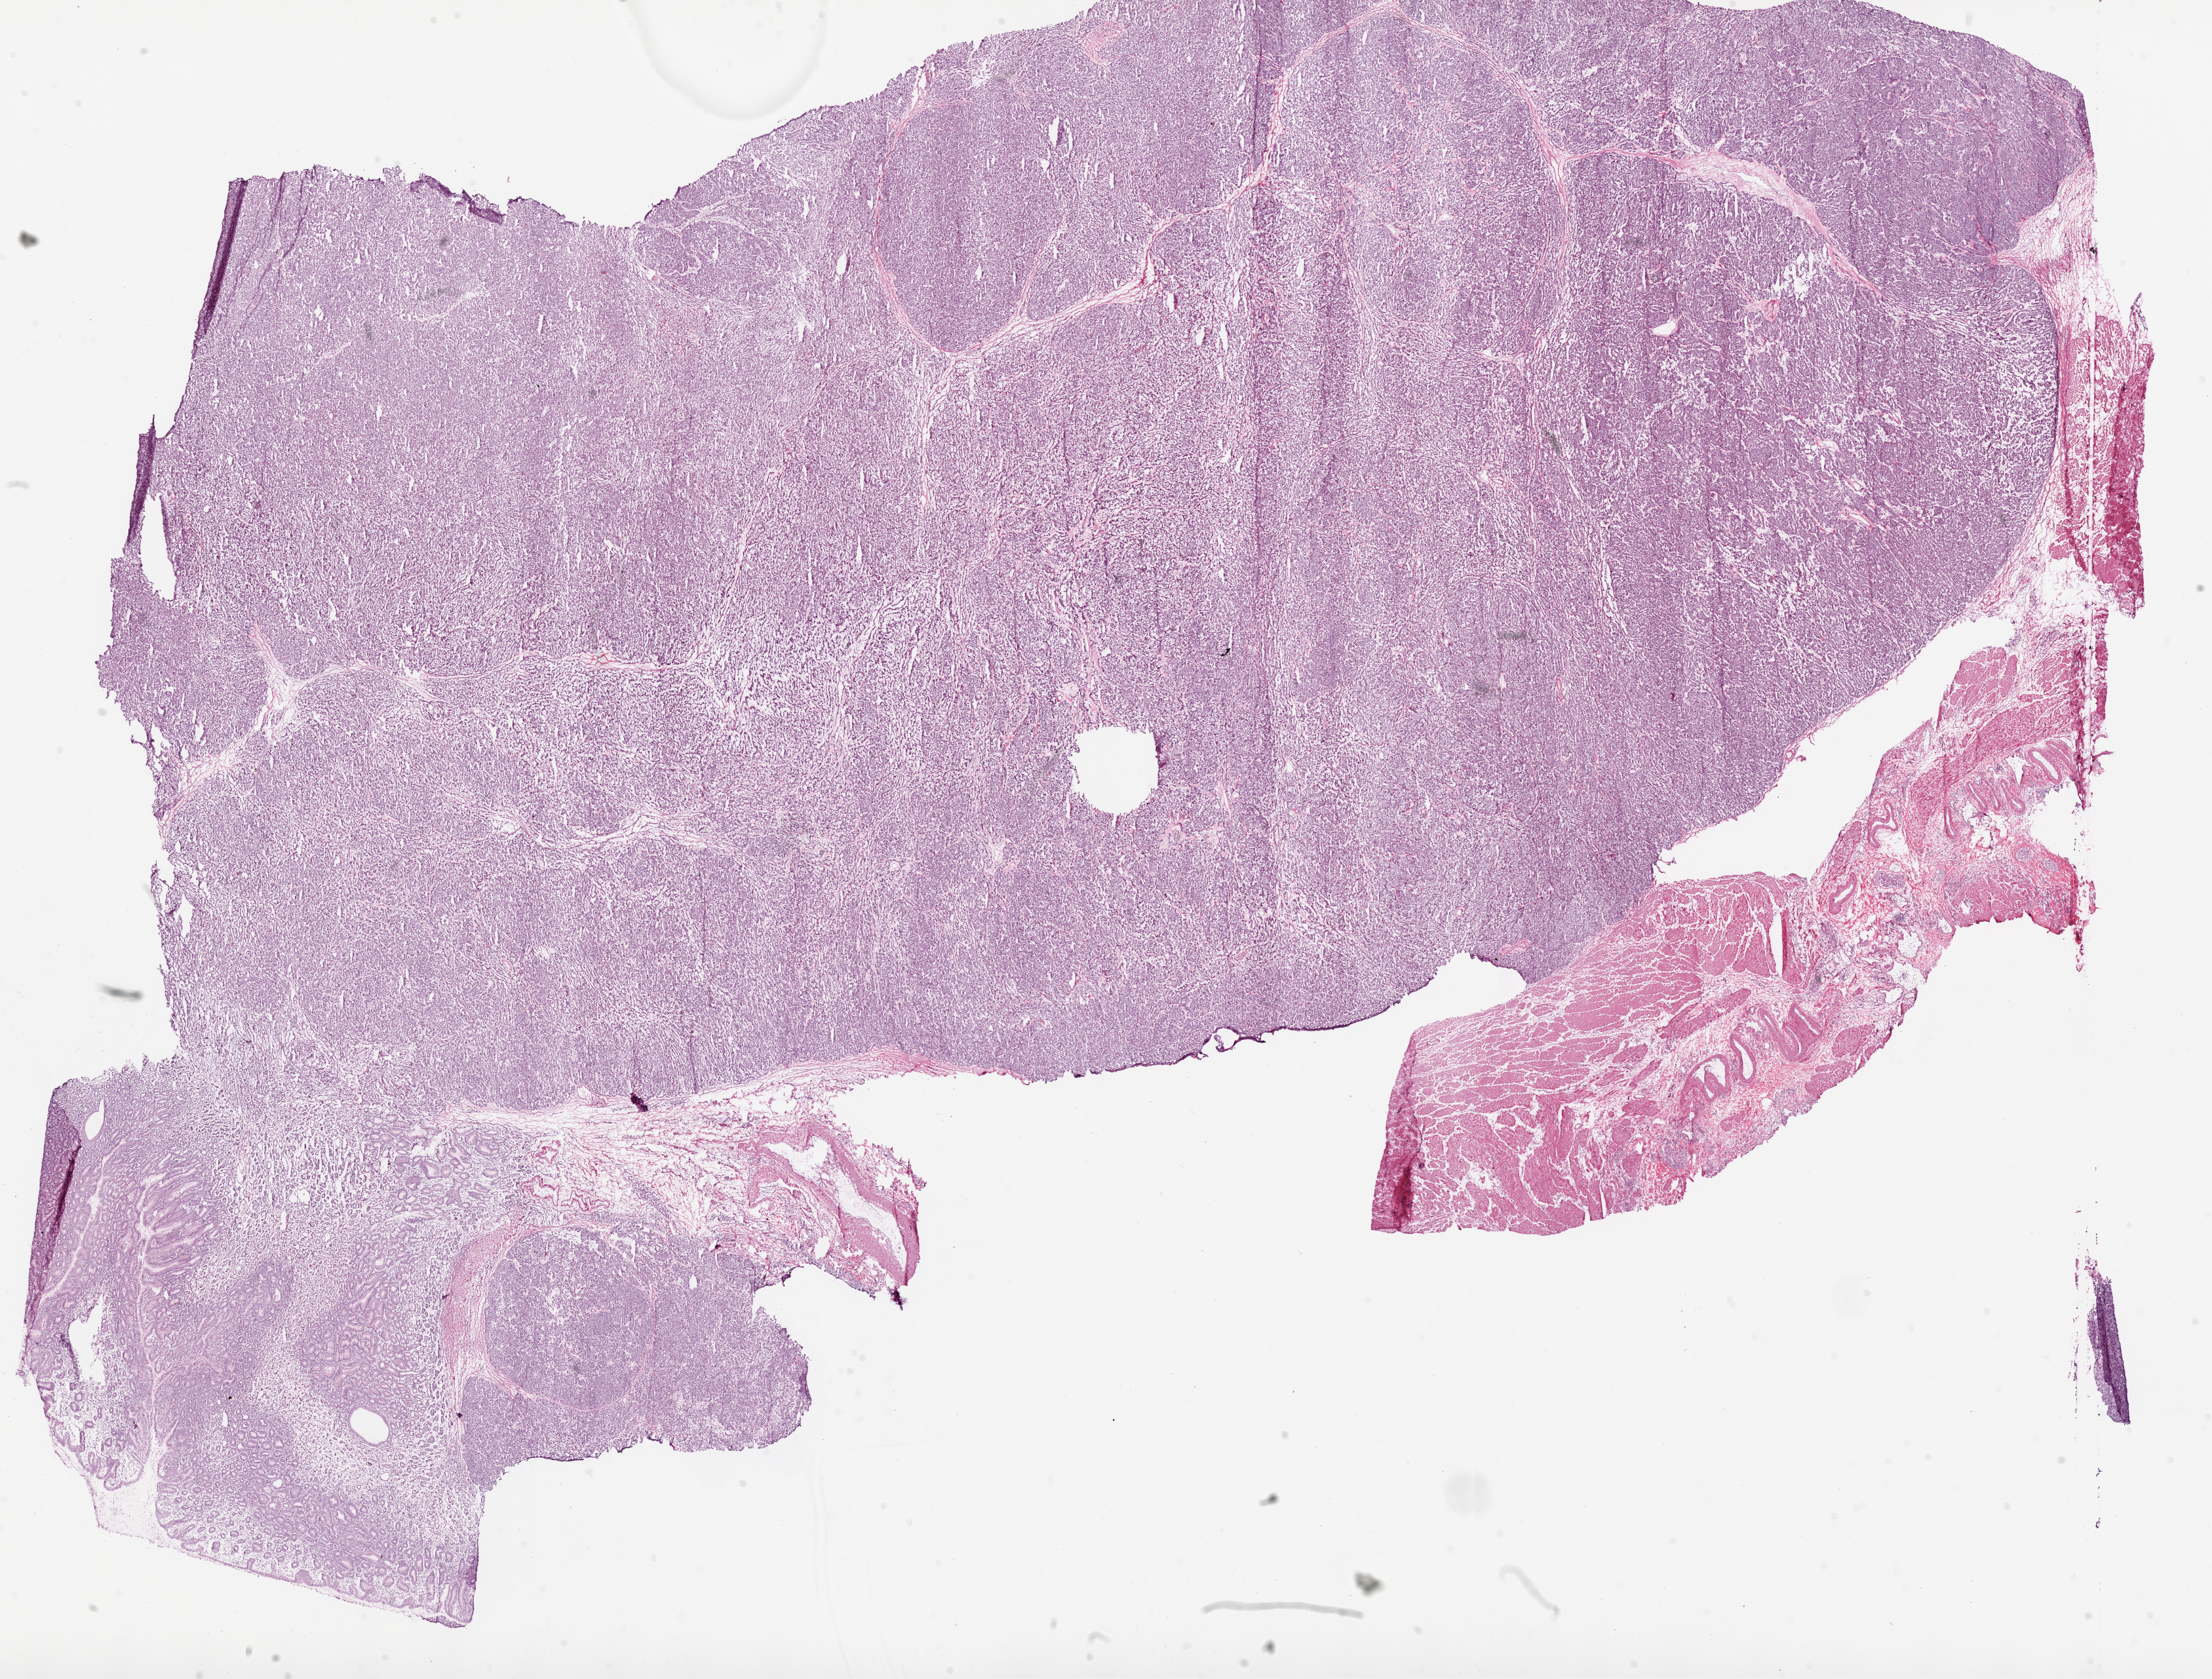
H&E whole-slide image — low-resolution overview of the scanned area, about 27.1 x 20.6 mm (acquisition: 20x scan), frozen section from the top of the tissue portion, sample: primary tumour, stomach. Male, age 65 years at initial diagnosis. Histologic grade: G2 (moderately differentiated). Slide review estimates, as recorded: tumour cells 86%, tumour nuclei 85%, normal cells 8%, stromal cells 5%, necrosis 1%.
• diagnosis: Tubular adenocarcinoma (body of stomach)